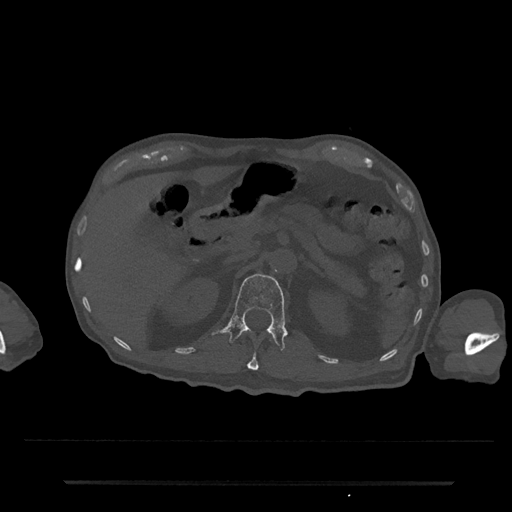
CT including the spine, one axial slice. Position 148 of 797 along the scan axis. 120 kVp. Bone window (W 1800 / L 400 HU). 0.5 mm slice thickness. 512 × 512 image matrix, field of view 427 × 427 mm. Patient: male, 74 years. Case-level facts recorded for this patient, not image findings: primary cancer: prostate.
Structures marked on this image (semi-automatically segmented with operator editing):
- L1 vertebra: bounding box <215,273,287,351> (left, top, right, bottom; pixels)
- T12 vertebra: <247,353,259,371>